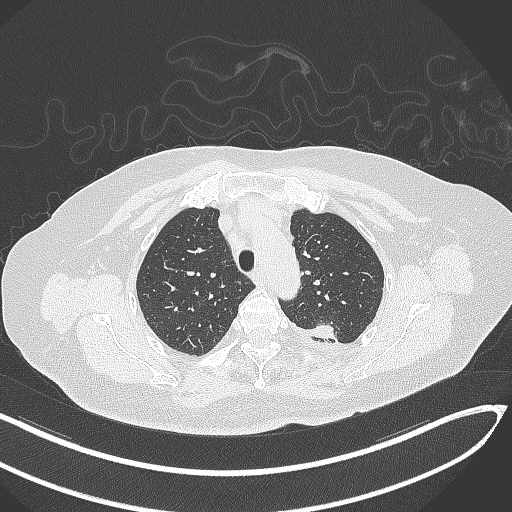
Chest CT, one axial slice; position 250 of 270 along the scan axis; reconstruction kernel B70f; 120 kVp; lung window (W 1500 / L -600 HU); 512 × 512 image matrix. Patient: female, 76 years. From the clinical record (not read from this slice): clinical TNM (as recorded): T1c N0 M0.
Structures marked on this image (bounding box drawn by a radiologist):
- lung tumour (recorded histology: adenocarcinoma): bounding box [x1, y1, x2, y2] px = [307, 320, 337, 343]